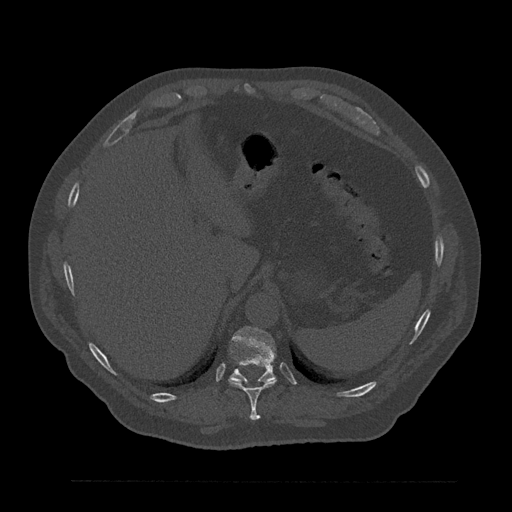
CT including the spine, one axial slice. Slice 324 of 797 in the series (ordered by position). Reconstruction kernel Br40s/3. Bone window (W 1800 / L 400 HU). 0.5 mm slice thickness. 512 × 512 image matrix. Male patient, age 61 years. From the clinical record (not read from this slice): primary cancer: prostate.
Structures marked on this image (semi-automatic segmentation, software-assisted and operator-edited):
- T10 vertebra: bounding box <228,379,277,420> (left, top, right, bottom; pixels)
- T11 vertebra: <230,326,276,383>